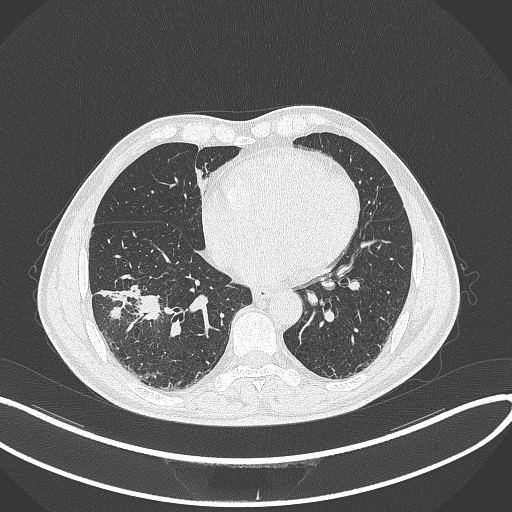
Chest CT, one axial slice; slice 133 of 364 in the series (ordered by position); reconstruction kernel B70f; 120 kVp; lung window (W 1500 / L -600 HU); 1 mm slice thickness; 512 × 512 image matrix. Patient: male, 58 years. Case-level facts recorded for this patient, not image findings: clinical TNM (as recorded): T3 N0 M0.
Structures marked on this image (bounding box drawn by a radiologist):
- lung tumour (recorded histology: squamous cell carcinoma): bounding box [x1, y1, x2, y2] px = [127, 292, 162, 325]